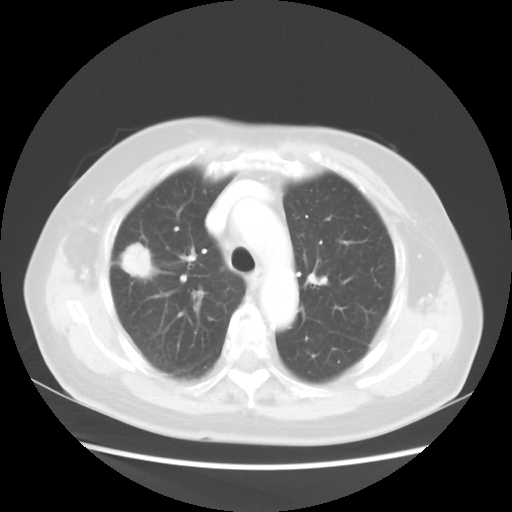
Chest CT, one axial slice; slice 34 of 48 in the series (ordered by position); reconstruction kernel STANDARD; lung window (W 1500 / L -600 HU); 512 × 512 image matrix, field of view 360 × 360 mm. Patient: female, 75 years. Case-level facts recorded for this patient, not image findings: clinical TNM (as recorded): T1c N0 M0.
Annotated regions visible in this slice (rectangle marked by the reading radiologist):
- lung tumour (recorded histology: adenocarcinoma): bounding box <119,239,153,284> (left, top, right, bottom; pixels)